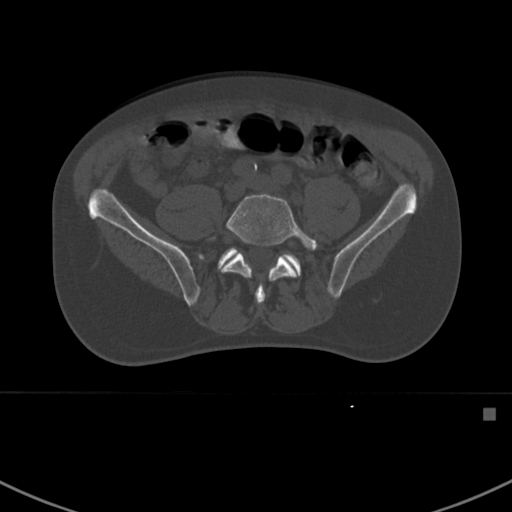
CT including the spine, one axial slice; position 216 of 412 along the scan axis; reconstruction kernel Br40s; 120 kVp; bone window (W 1800 / L 400 HU); 1.5 mm slice thickness; 512 × 512 image matrix, field of view 358 × 358 mm. Male patient, age 59 years. Case-level facts recorded for this patient, not image findings: primary cancer: prostate.
Annotated regions visible in this slice (semi-automatic segmentation, software-assisted and operator-edited):
- L5 vertebra: bounding box (x1, y1, x2, y2) in pixels: (207, 193, 318, 304)